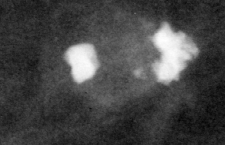
Cropped region of a digitized screen-film mammogram centred on a radiologist-marked abnormality; left breast; CC view.
Calcifications, morphology coarse; BI-RADS assessment category 2; benign; no additional work-up was recommended (benign without callback).